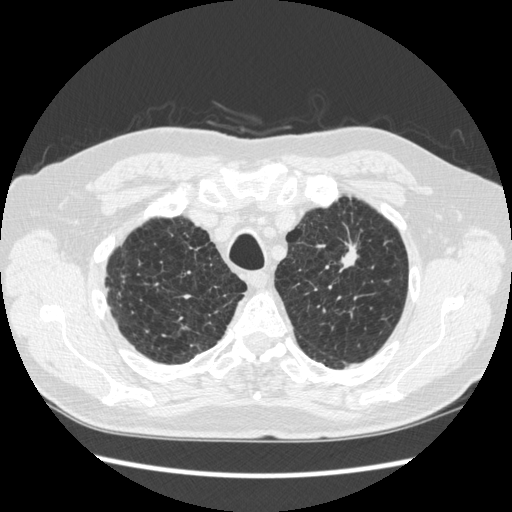
Chest CT (low-dose screening protocol), one axial image, third screening round (two years after baseline), lung window (W 1500 / L -600 HU), 1.25 mm slice thickness, 120 kVp, slice 44 of 267 in the series, 512 × 512 image matrix. Male, age 70 years at enrolment.
Lesion marked by an expert reader, bounding box [x1, y1, x2, y2] px = [323, 219, 374, 284]. The screening reader recorded 2 non-calcified nodules or masses ≥4 mm on this exam; which of them this box marks is not recorded. Participant outcome: lung cancer diagnosed 92 days after this screen — squamous cell carcinoma, NOS, left upper lobe, moderately differentiated (G2), stage IA (AJCC 6th edition), 18 mm at pathology.